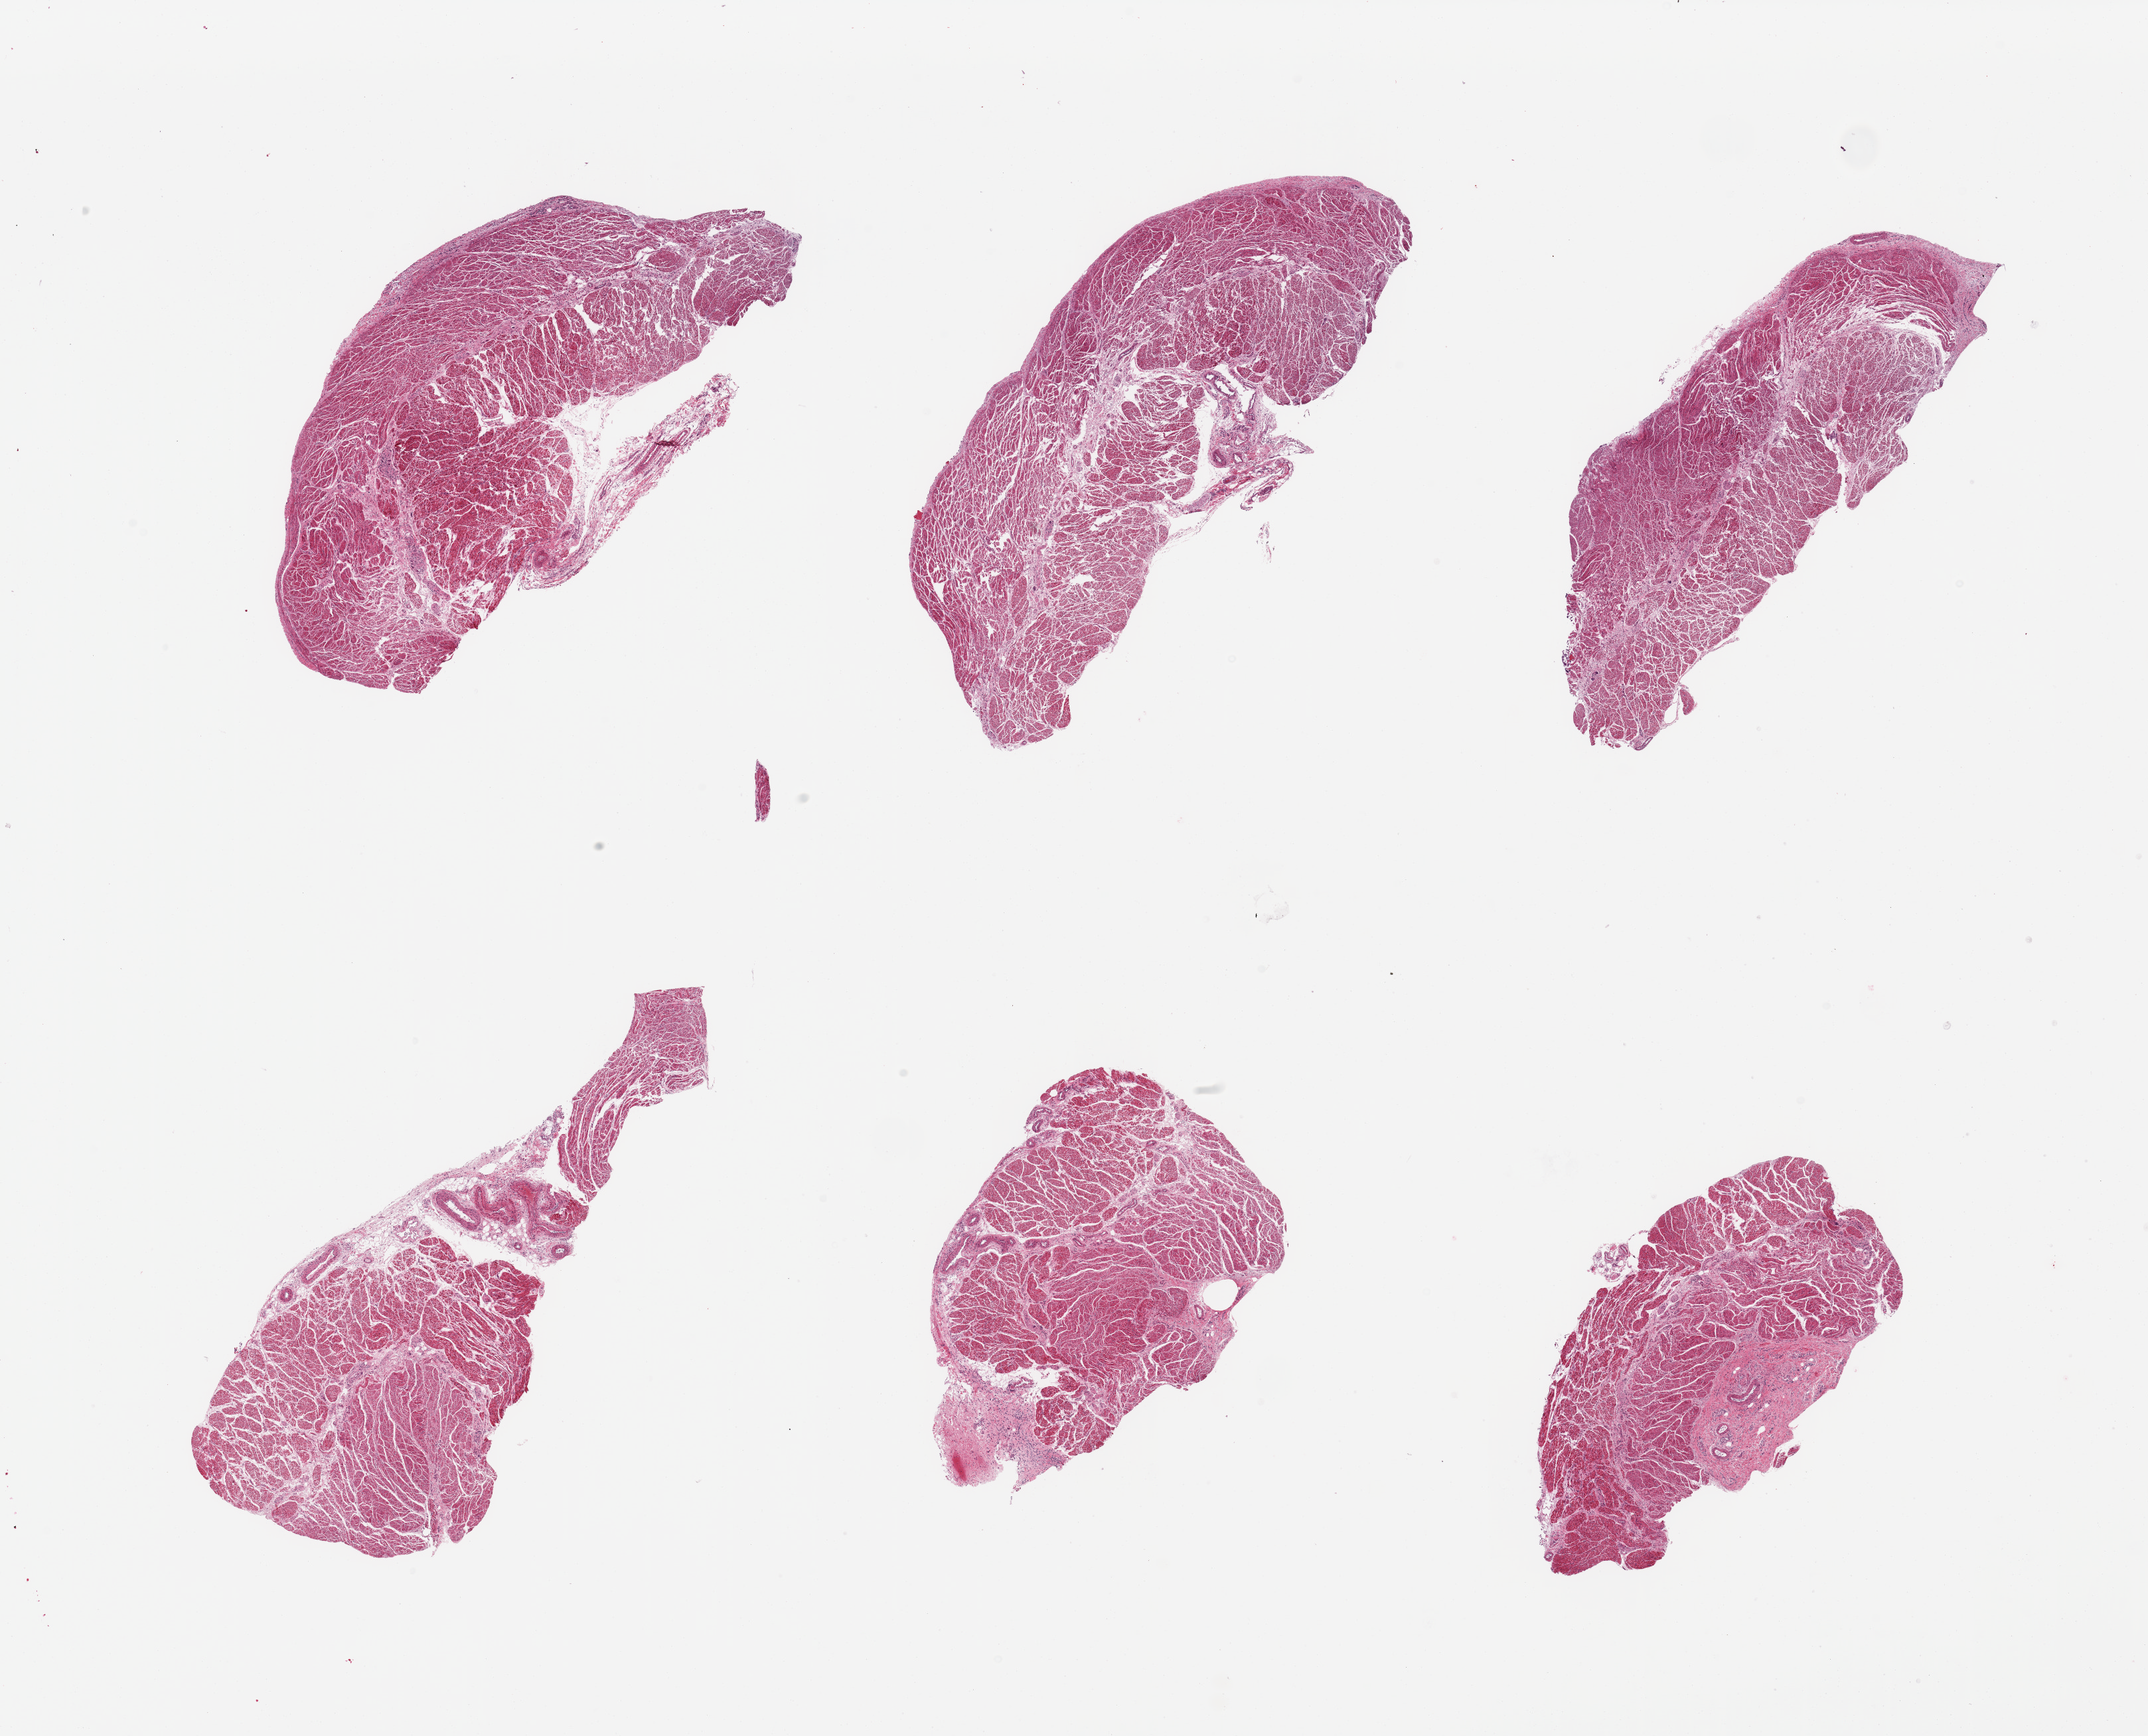
Hematoxylin and eosin (H&E) whole-slide image, a low-resolution overview of the entire scanned area, about 25.6 x 20.7 mm (slide scanned at 20x). PAXgene-fixed, paraffin-embedded tissue. Target tissue: esophageal muscle. Donor tissue sample.
* reviewer comment on this tissue sample: 6 pieces; submucosal remnant [20%] on 1 piece